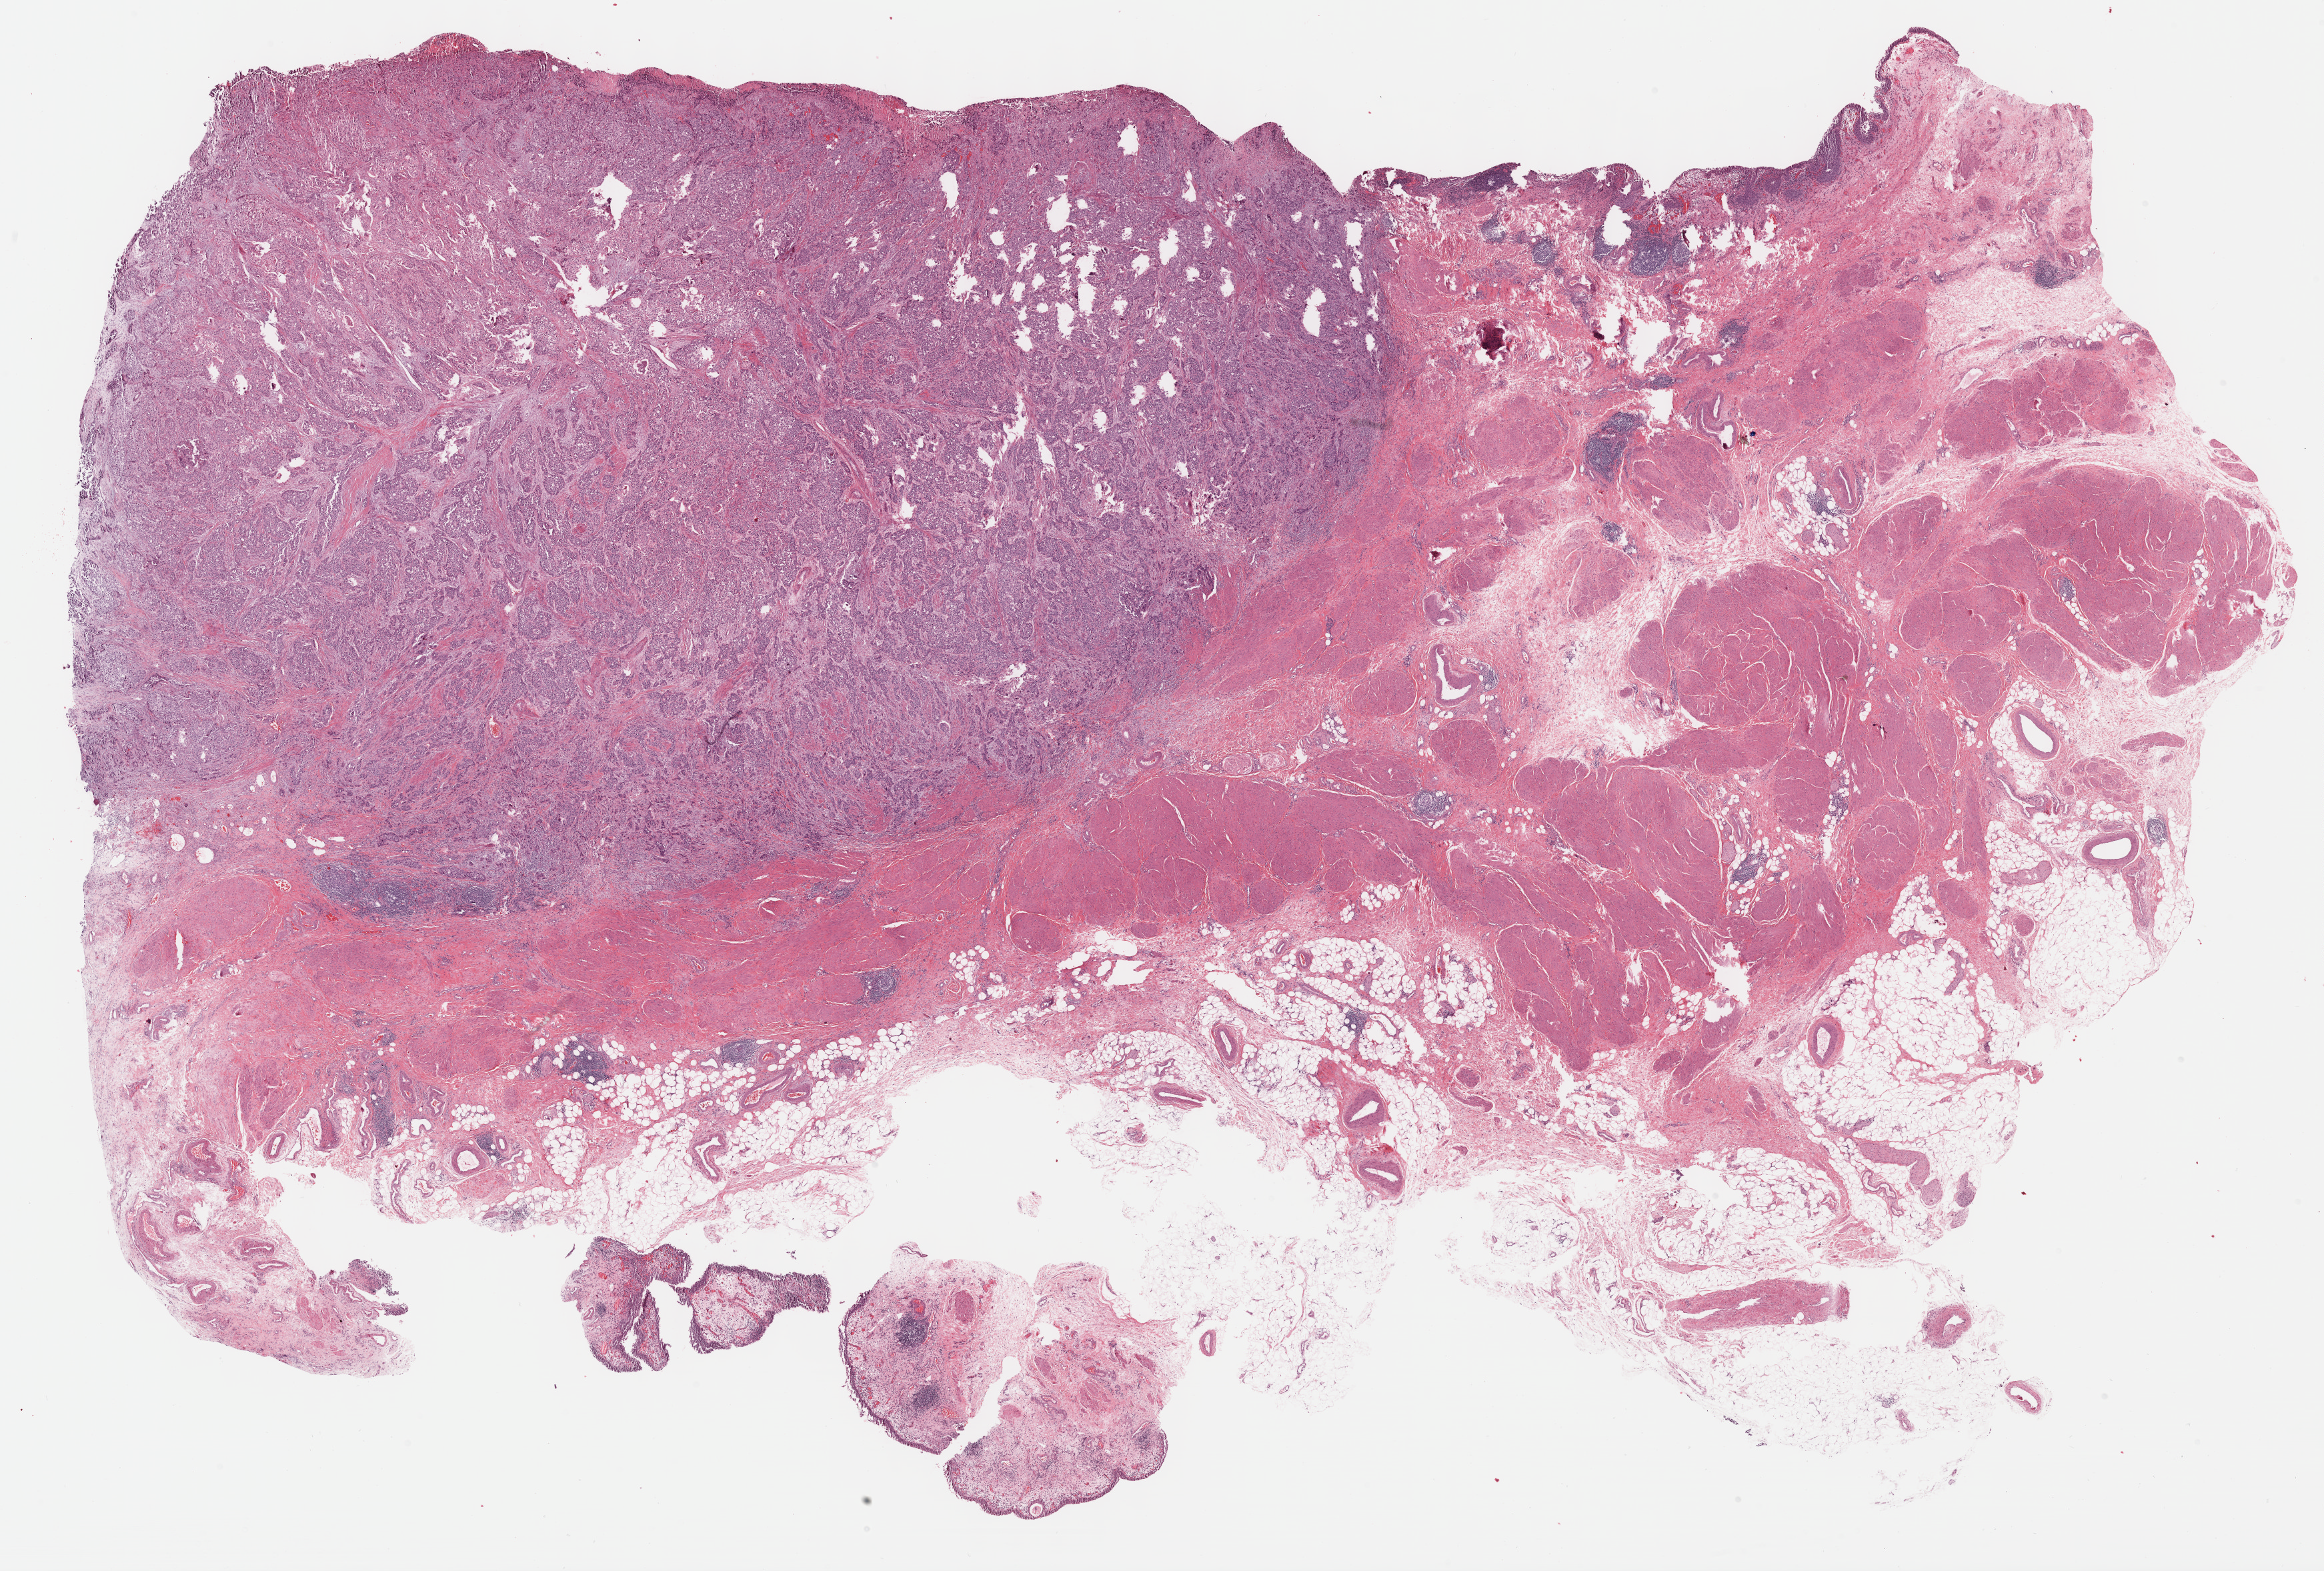
Whole-slide histology image, Hematoxylin and eosin (H&E) stained — a low-resolution overview of the entire scanned area, about 28.2 x 19.1 mm (slide scanned at 40x). Formalin-fixed paraffin-embedded (FFPE) diagnostic section. Primary tumour sample from the bladder. Patient: male, age at initial diagnosis 81 years. Histologic grade: high grade.
Histologic diagnosis: Transitional cell carcinoma (trigone of bladder). AJCC pathologic stage: IV.